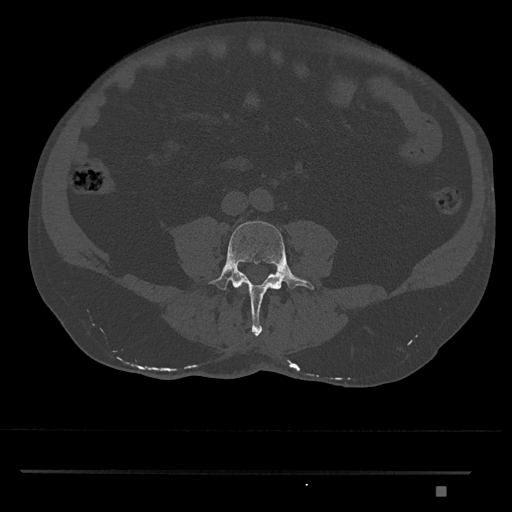
CT including the spine, one axial slice; position 619 of 1134 along the scan axis; reconstruction kernel Br40s/3; 120 kVp; bone window (W 1800 / L 400 HU); 0.5 mm slice thickness; 512 × 512 image matrix, field of view 429 × 429 mm. Male patient, age 65 years. Case-level facts recorded for this patient, not image findings: primary cancer: prostate.
Annotated regions visible in this slice (semi-automatically segmented with operator editing):
- L4 vertebra: bounding box <207,221,314,336> (left, top, right, bottom; pixels)